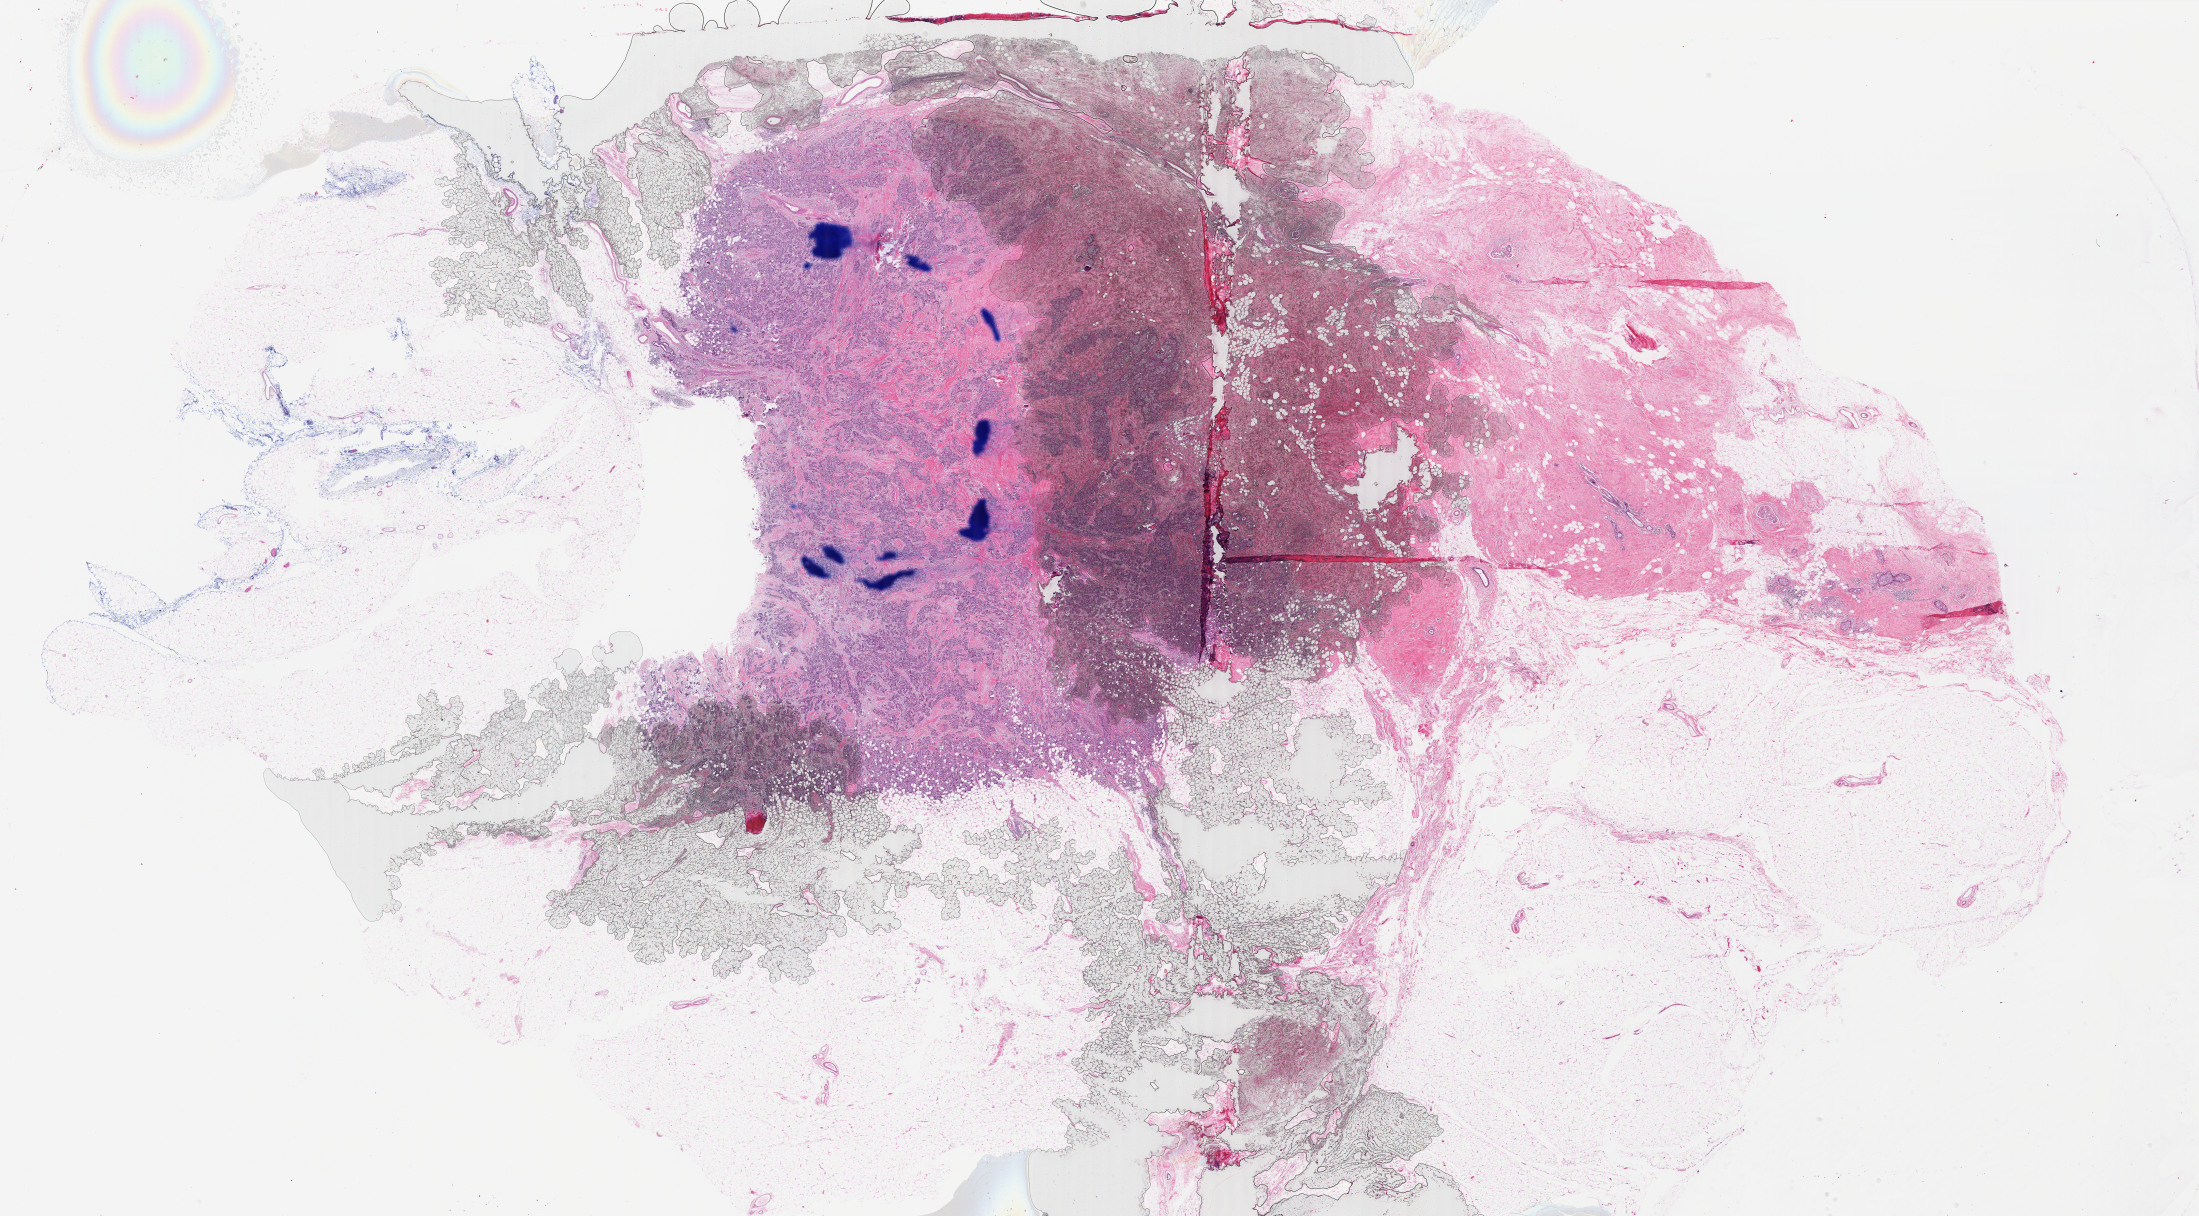
Digitized H&E-stained tissue section (whole slide) — low-resolution overview of the scanned area, about 35.0 x 19.3 mm. Formalin-fixed paraffin-embedded (FFPE) diagnostic section. Sample: primary tumour, breast. Patient: female, age at initial diagnosis 73 years.
Laterality: left. Diagnosis: Infiltrating duct and lobular carcinoma.